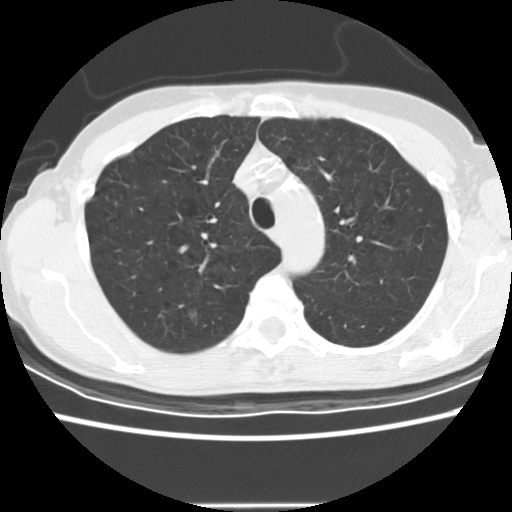
Chest CT (low-dose screening protocol), one axial image. Second screening round (one year after baseline). Lung window (W 1500 / L -600 HU). 2.5 mm slice thickness. Slice 39 of 166 in the series. Female participant, aged 58 years at enrolment.
- Lesion marked by an expert reader, bounding box [x1, y1, x2, y2] px = [174, 301, 209, 330].
- The screening reader recorded 2 non-calcified nodules or masses ≥4 mm on this exam; which of them this box marks is not recorded.
- Lung cancer was diagnosed 434 days after this screen (after the third annual screen): bronchiolo-alveolar adenocarcinoma, NOS, right upper lobe, well differentiated (G1), stage IA (AJCC 6th edition), 8 mm at pathology.